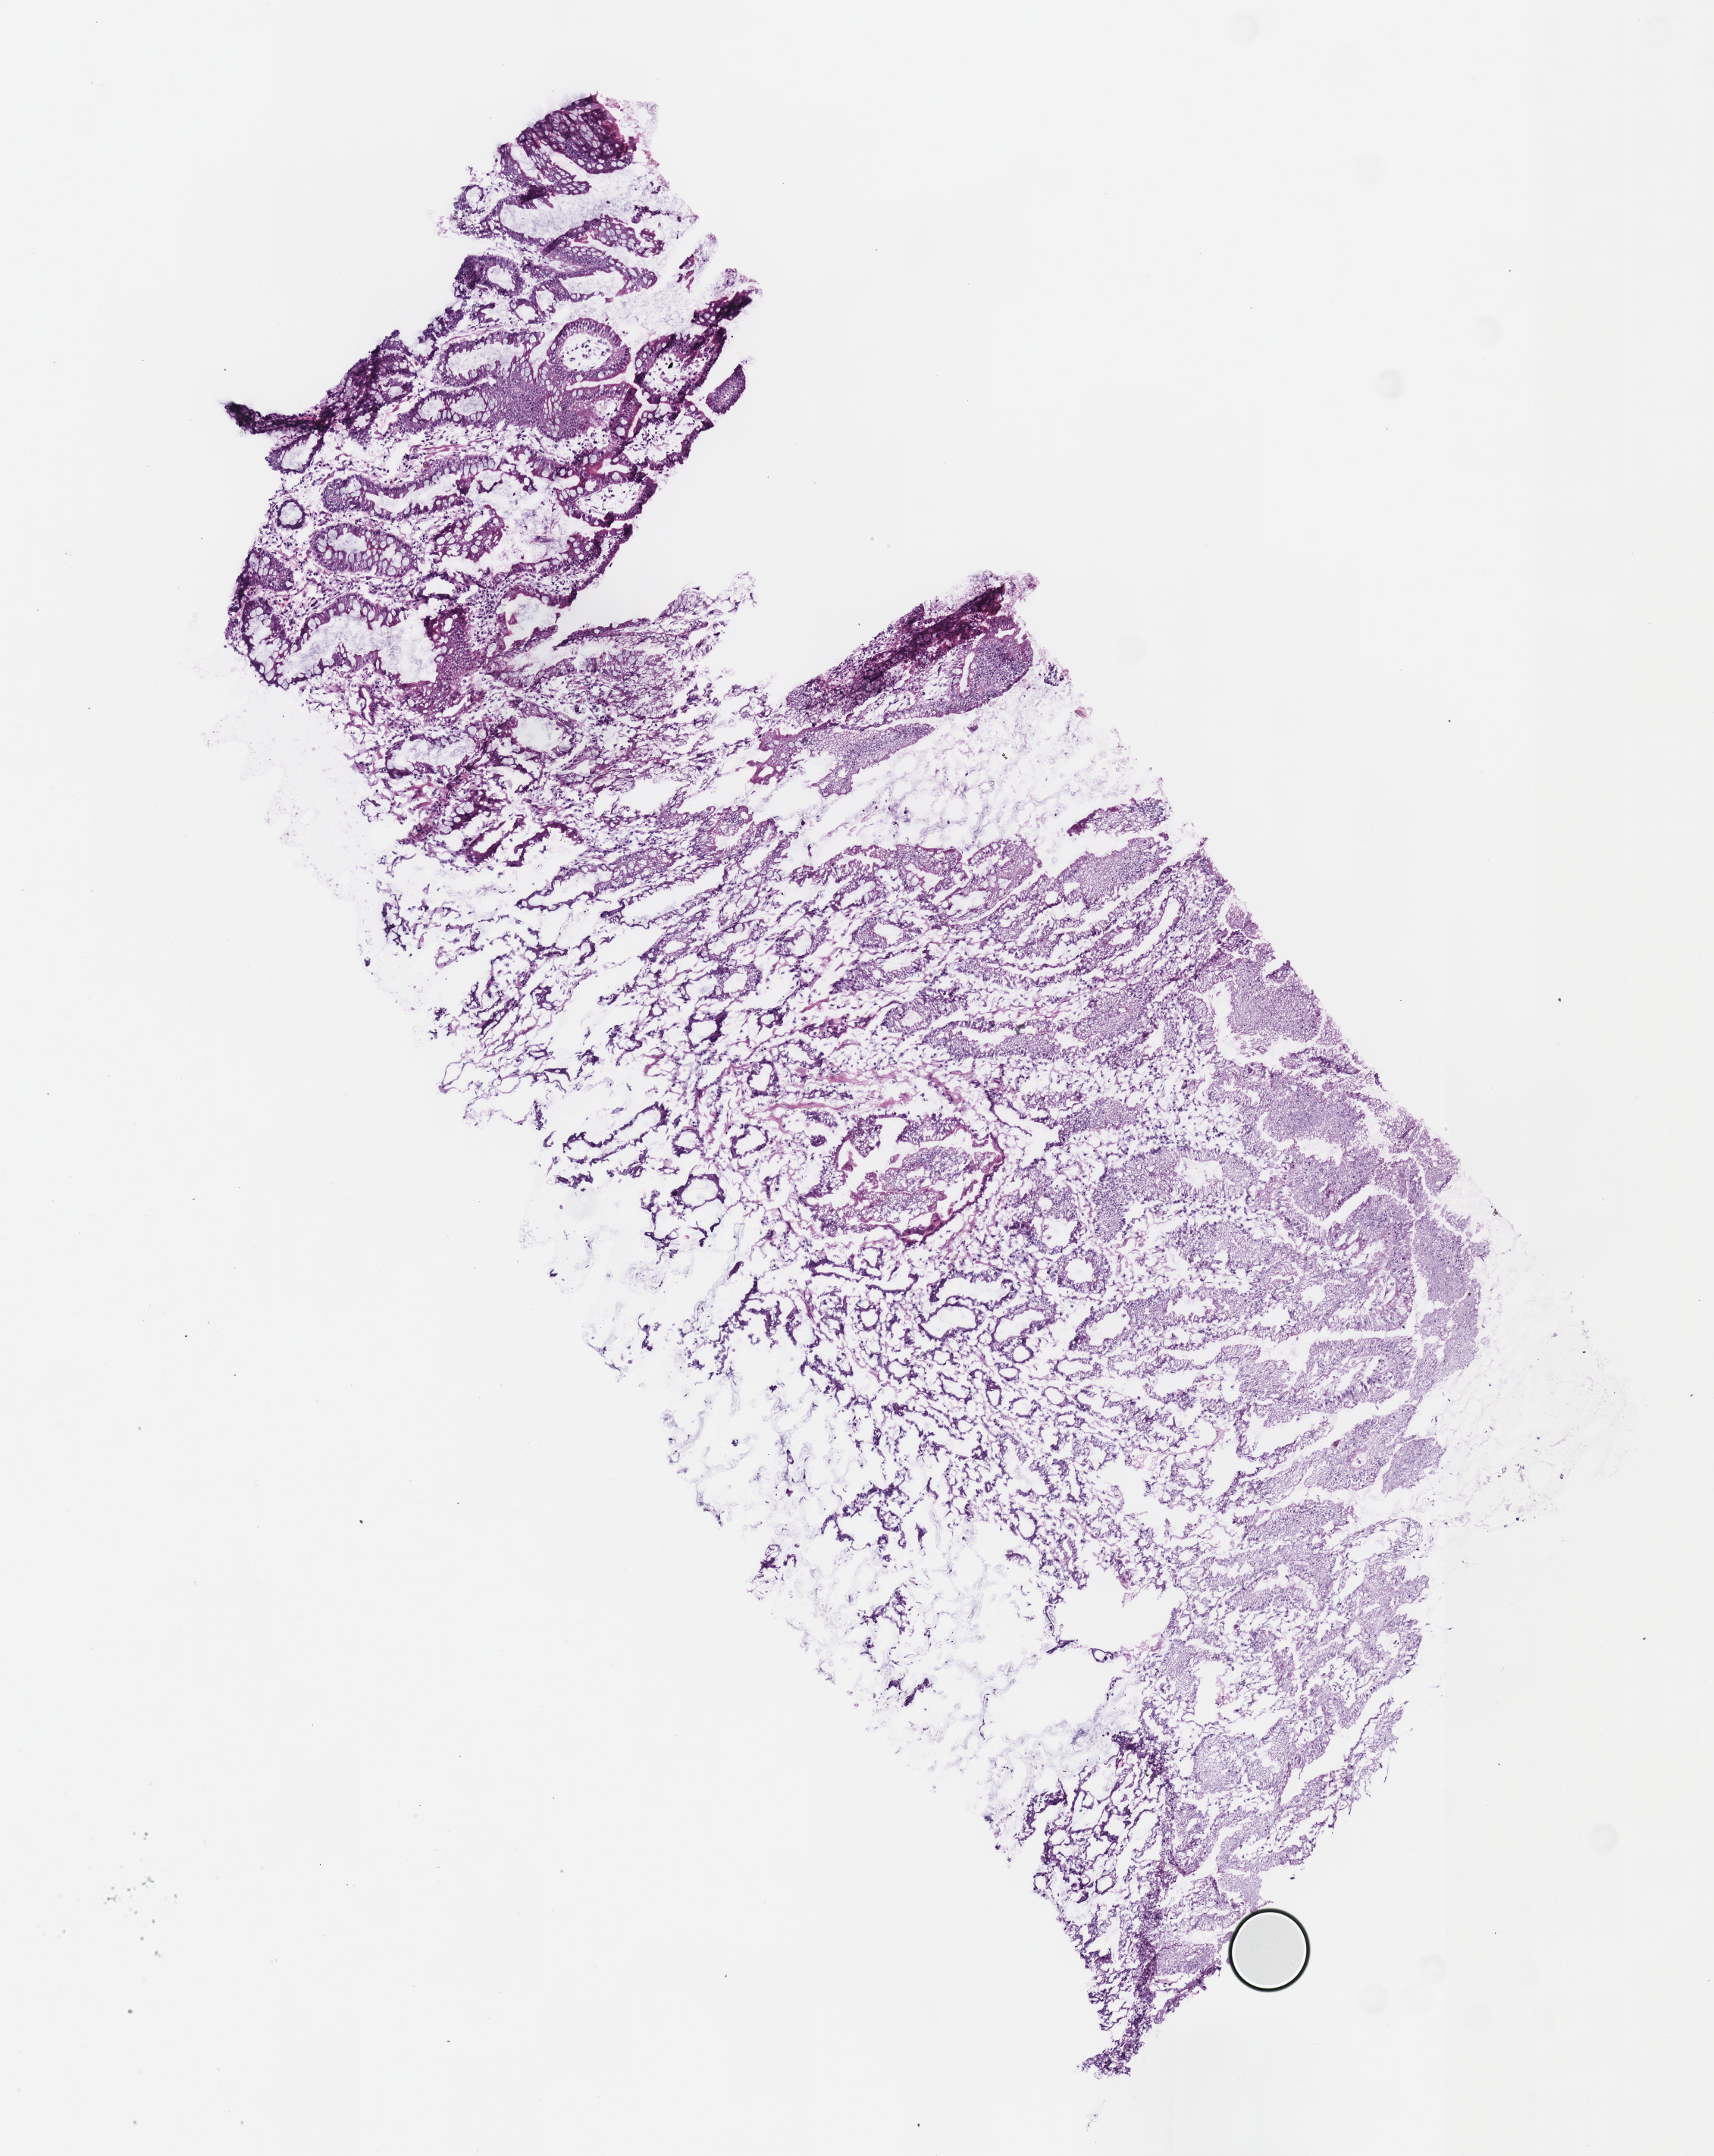
Whole-slide histology image, H&E-stained — whole scanned area (about 4.5 x 5.6 mm, acquisition: 40x scan) shown as a low-resolution overview. Frozen section. Primary tumour sample from the stomach. Patient: male, age at initial diagnosis 56 years. Histologic grade: G2 (moderately differentiated). Slide review estimates, as recorded: tumour cells 70%, tumour nuclei 70%, normal cells 20%, stromal cells 10%, necrosis 0%.
Pathologic diagnosis: Tubular adenocarcinoma (gastric antrum). Lymph nodes positive (case pathology): 1 of 46 examined.